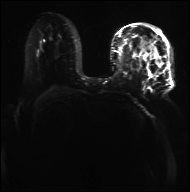
Breast MRI, one axial slice. Slice 16 of 36 in the series (ordered by position). Diffusion-weighted series; image 2 of 4 stored at this slice position (different b-values; order by instance number). 3 T. 4 mm slice thickness. 190 × 192 image matrix, field of view 317 × 320 mm. Female patient.
Outlined on this slice (outlined manually by an expert reader):
- tumour on diffusion-weighted imaging: bounding box (x1, y1, x2, y2) in pixels: (28, 40, 71, 66)